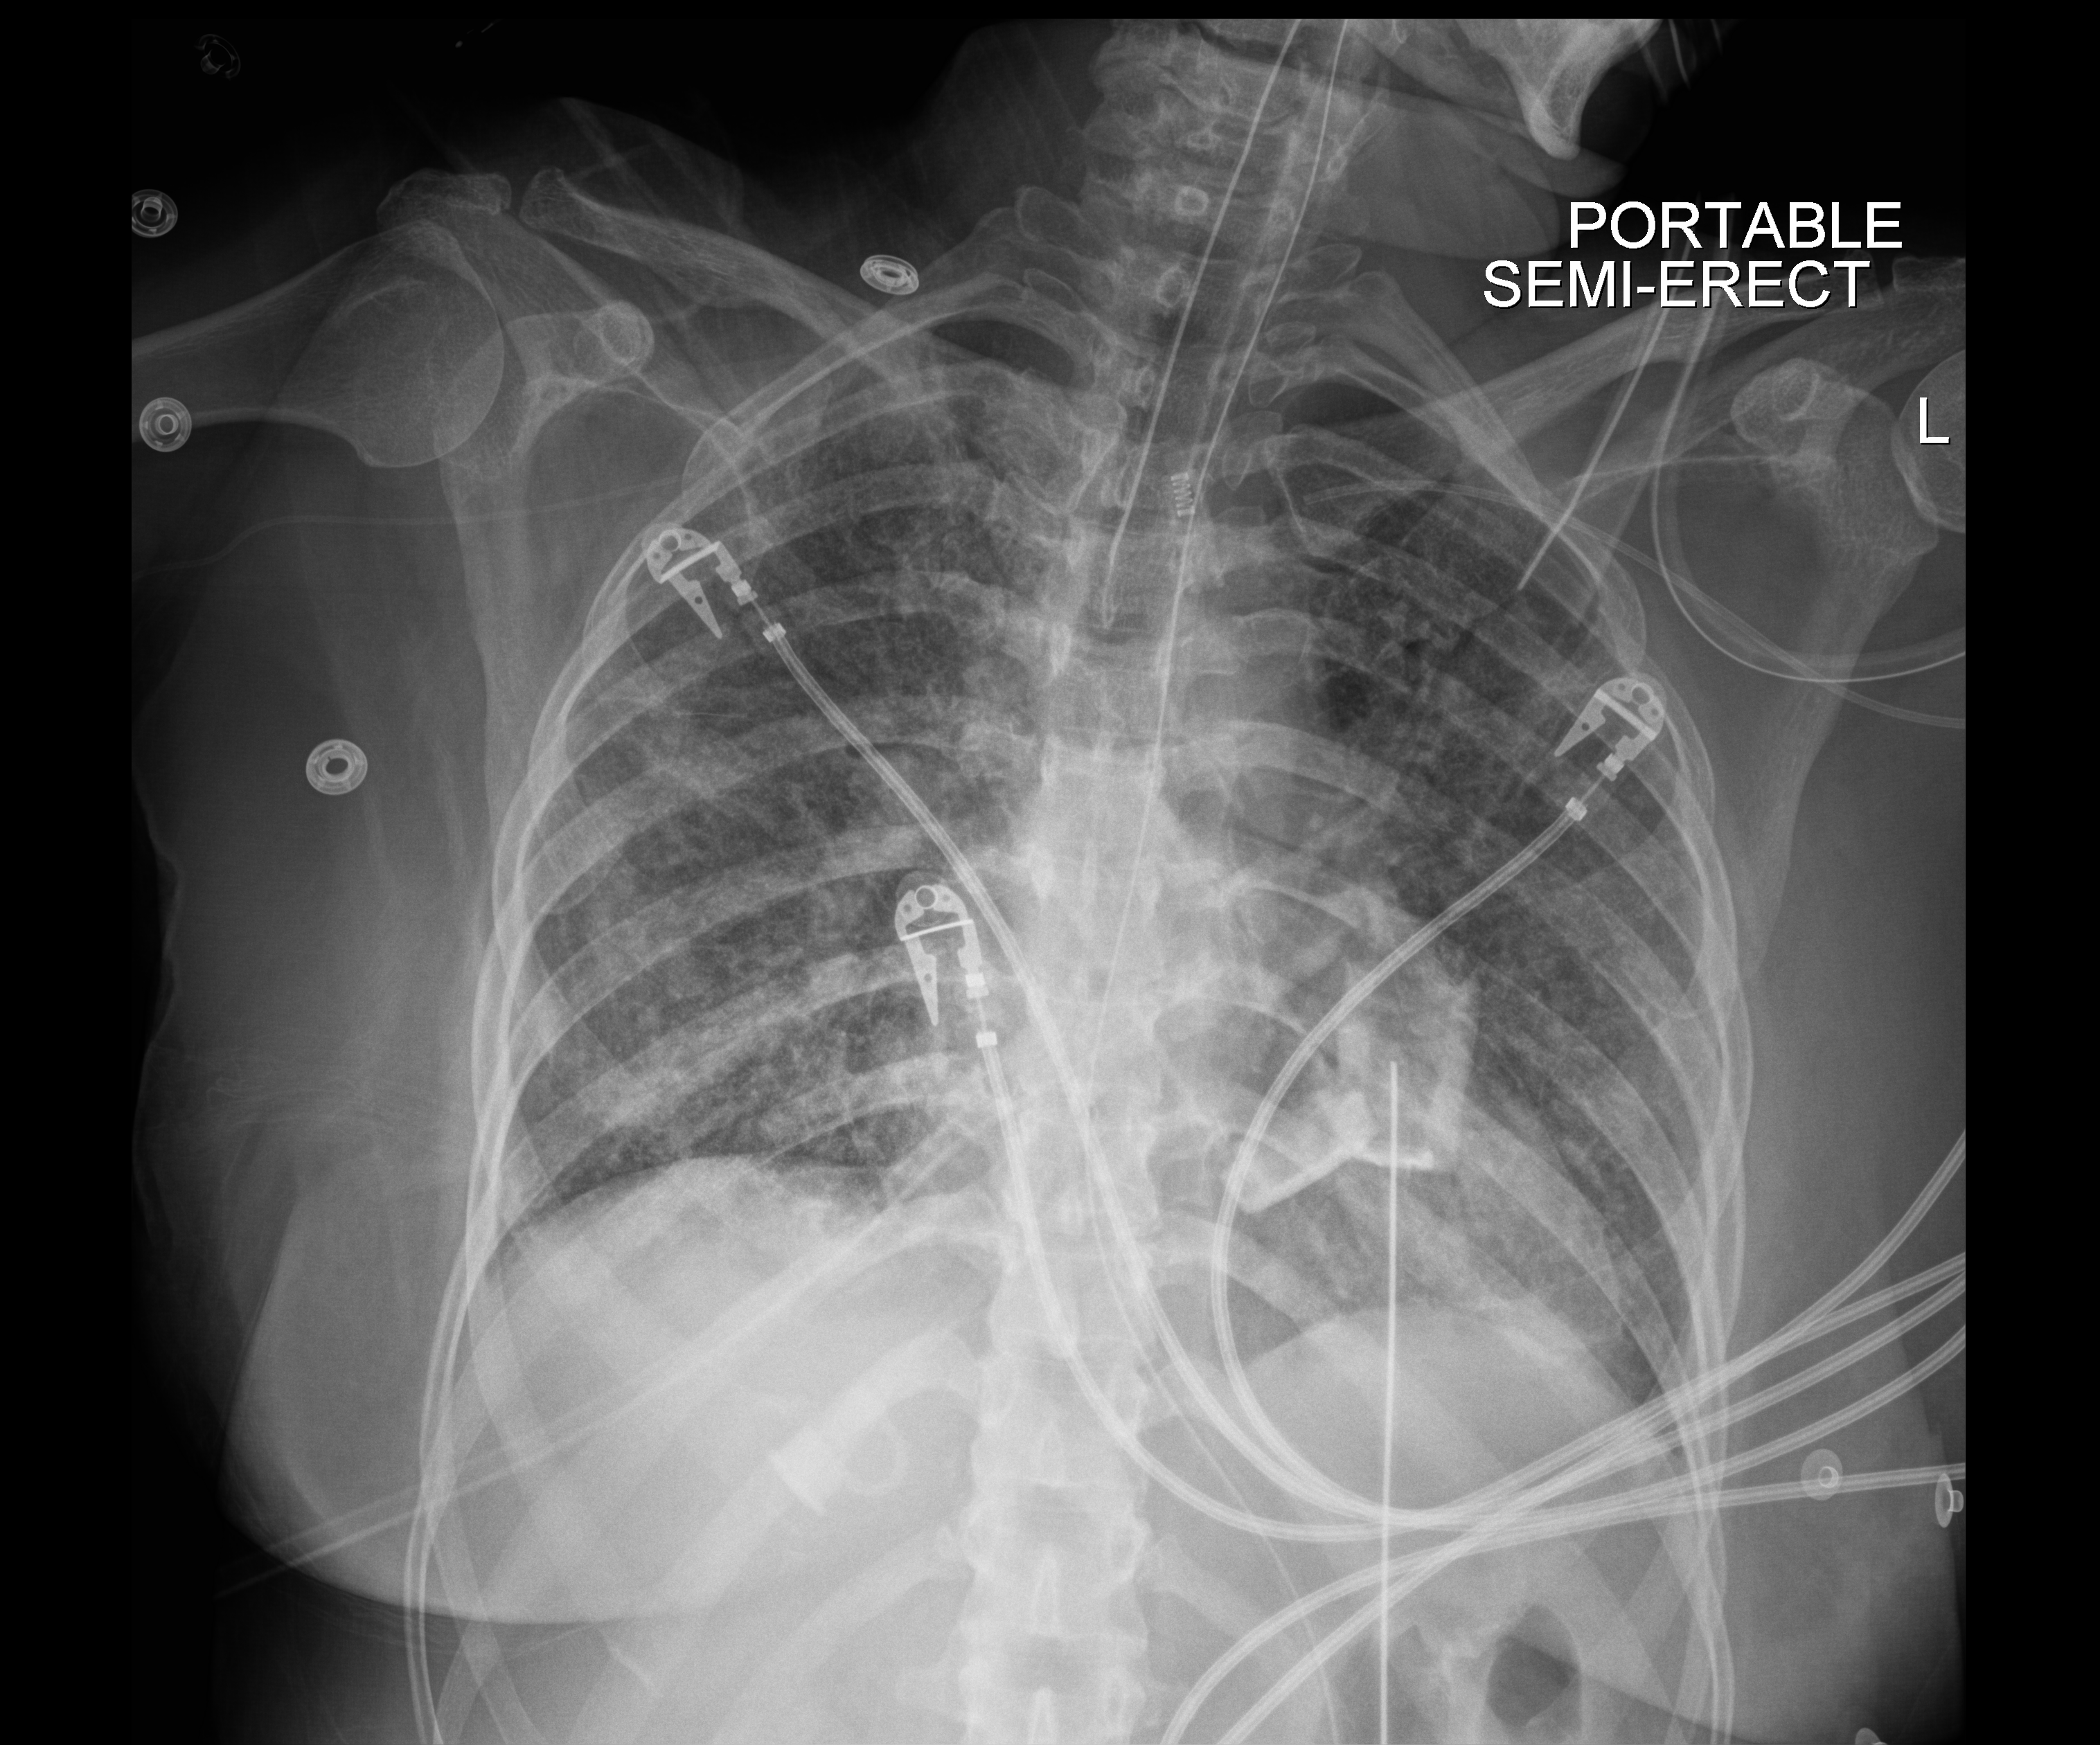
Chest X-ray (portable); anteroposterior (AP) projection. Male patient hospitalised with COVID-19, age 18–59 years.
Hospital-stay facts (about this admission, not read from this image; timing relative to this image not recorded):
- admitted to intensive care during this hospital stay: yes